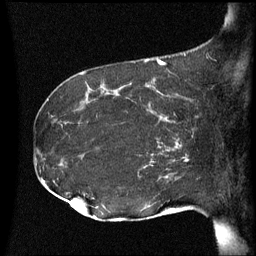
Breast MRI (dynamic contrast-enhanced), one sagittal slice. Slice 27 of 60 in the series (ordered by position). Dynamic contrast-enhanced series, image 2 of 3 at this slice position (ordered by acquisition). 1.5 T. TE 4.2 ms, TR 8.4 ms. 2.5 mm slice thickness. 256 × 256 image matrix. Patient: female, 41 years. Case-level facts recorded for this patient, not image findings: setting: breast cancer imaged before/during neoadjuvant chemotherapy; receptor status: HER2-positive.
Annotated regions visible in this slice (semi-automatically segmented with operator editing):
- analysis volume of interest (the breast-tissue region the enhancement analysis was run in; not a lesion): bounding box [x1, y1, x2, y2] px = [122, 84, 195, 137]
- tumour enhancement mask (voxels above the 70 % enhancement threshold inside the analysis volume of interest): [145, 84, 170, 123]